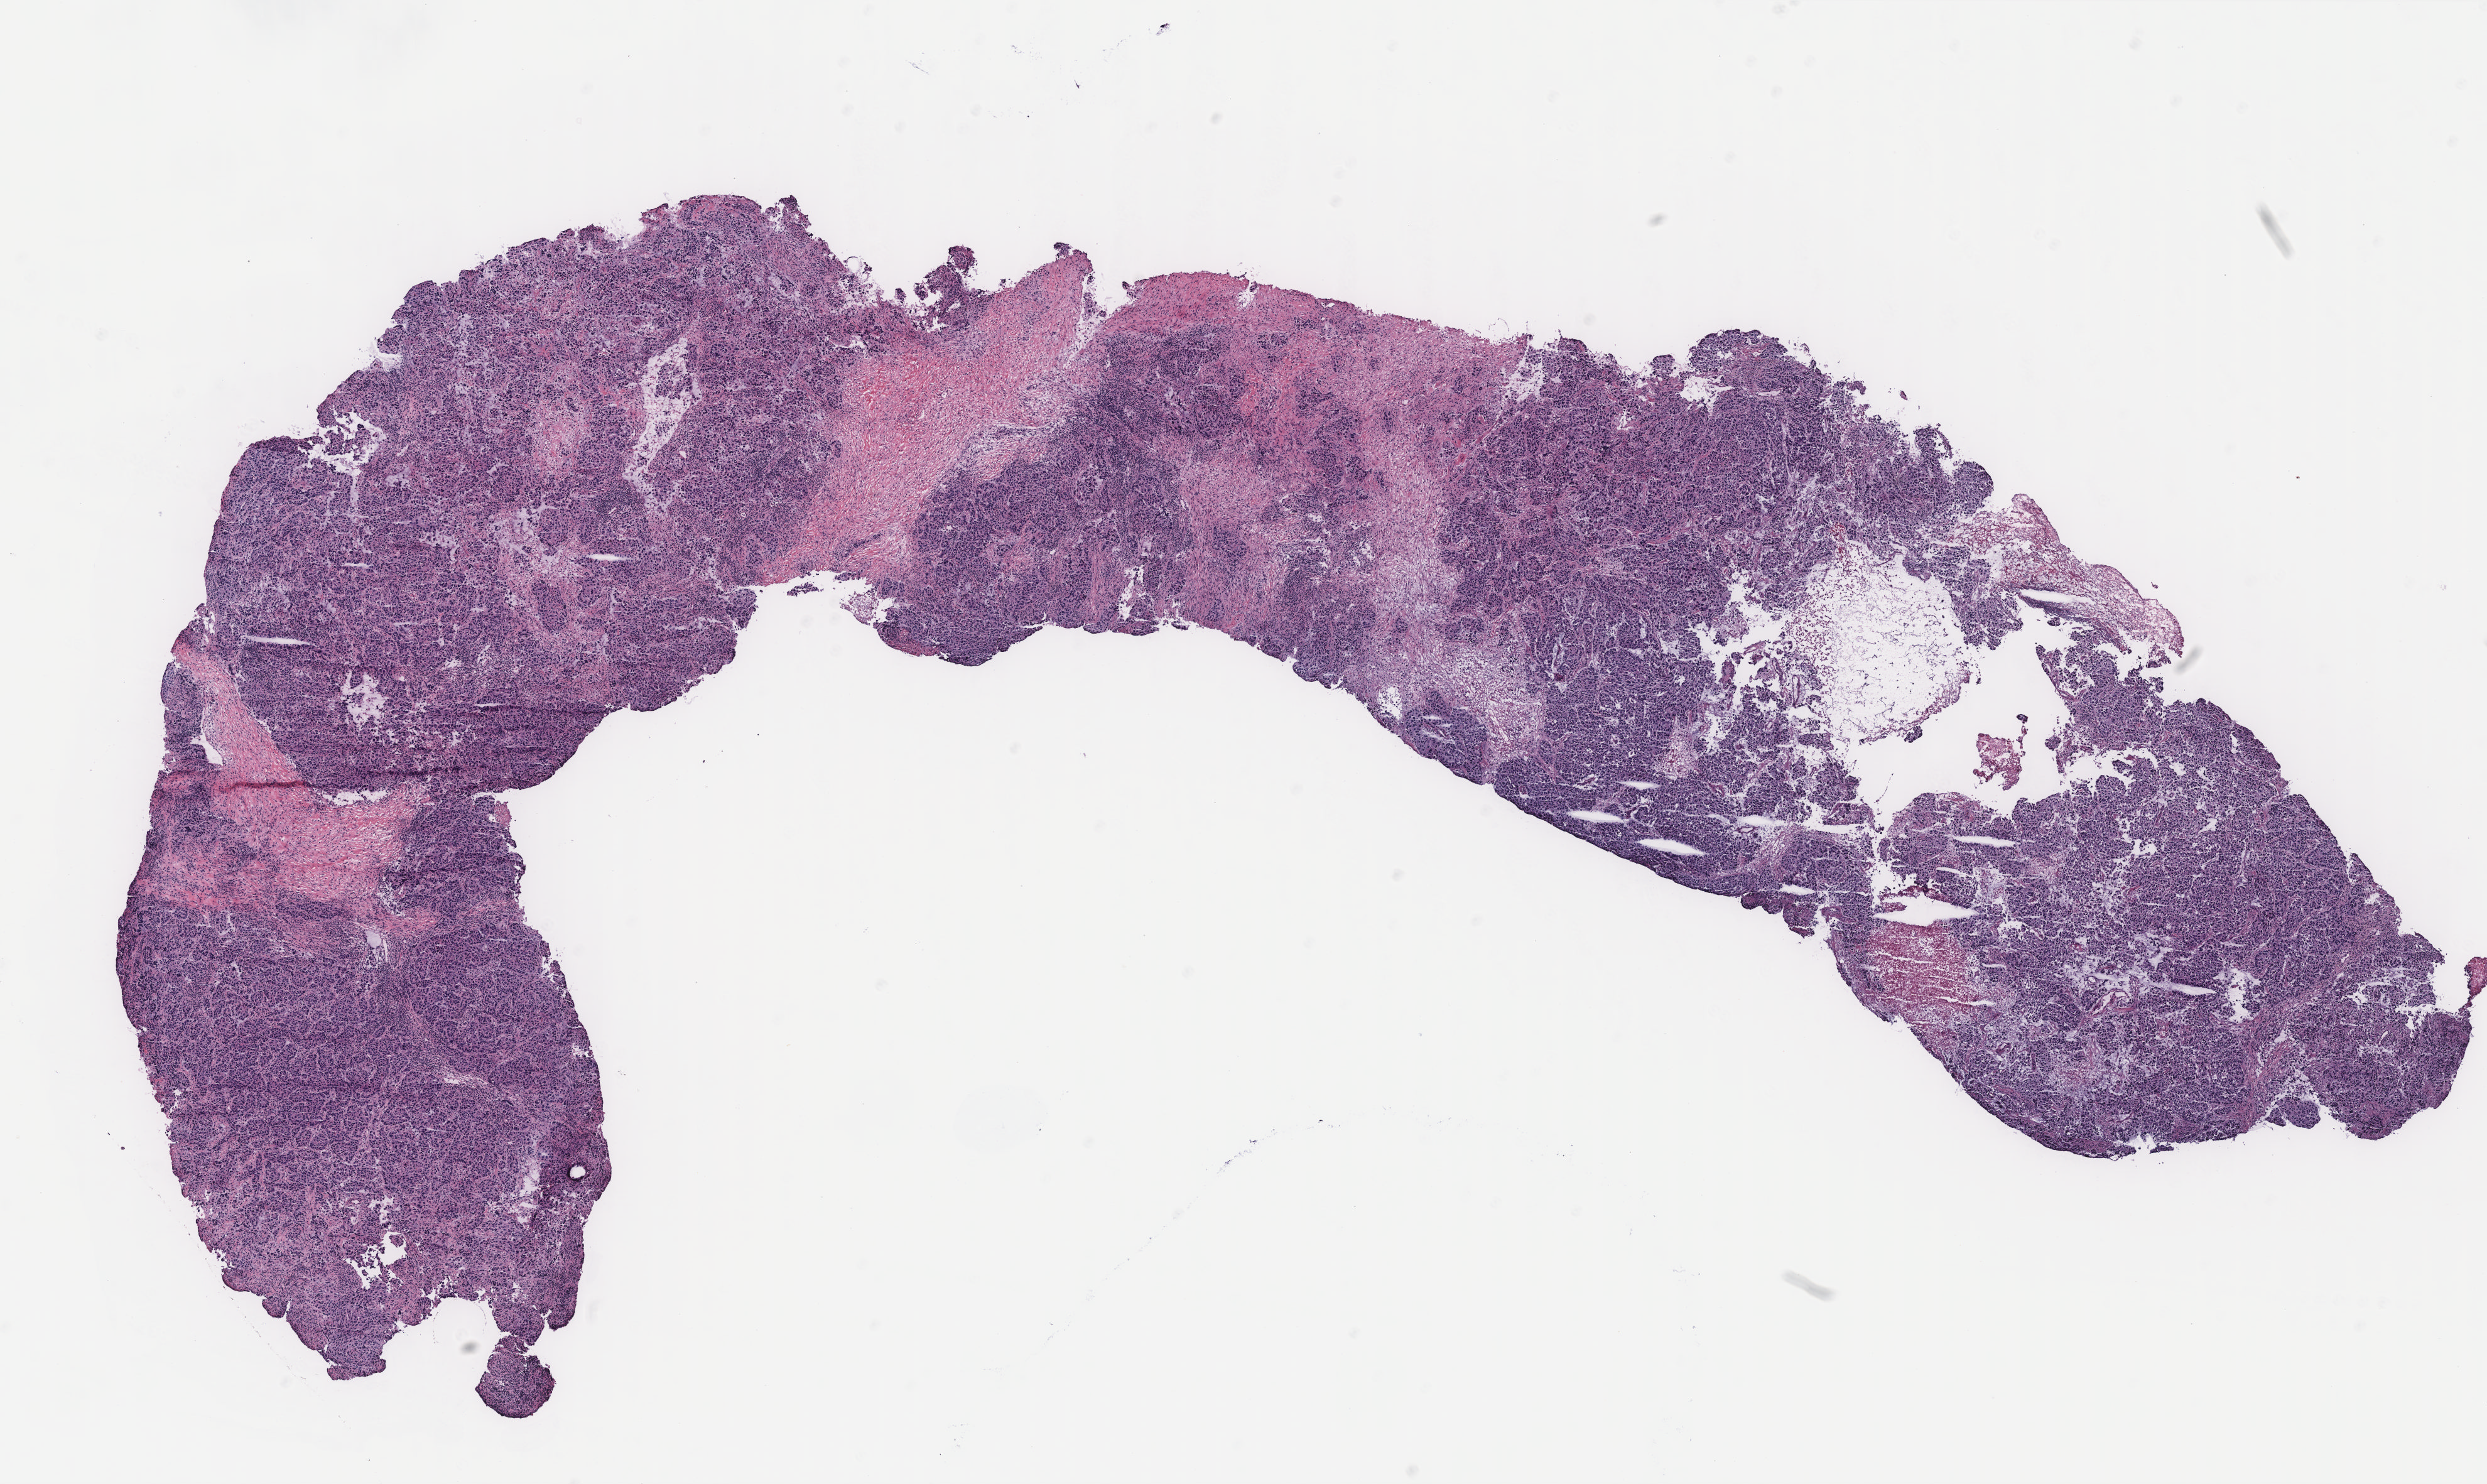
Digitized H&E tissue section (whole slide) — shown as a low-resolution overview of the whole scanned area (about 15.8 x 9.5 mm, from a 40x scan), breast, tumour tissue. Patient: female, age 80 years.
AJCC pathologic stage: IIA. Diagnosis: Infiltrating duct carcinoma, NOS.